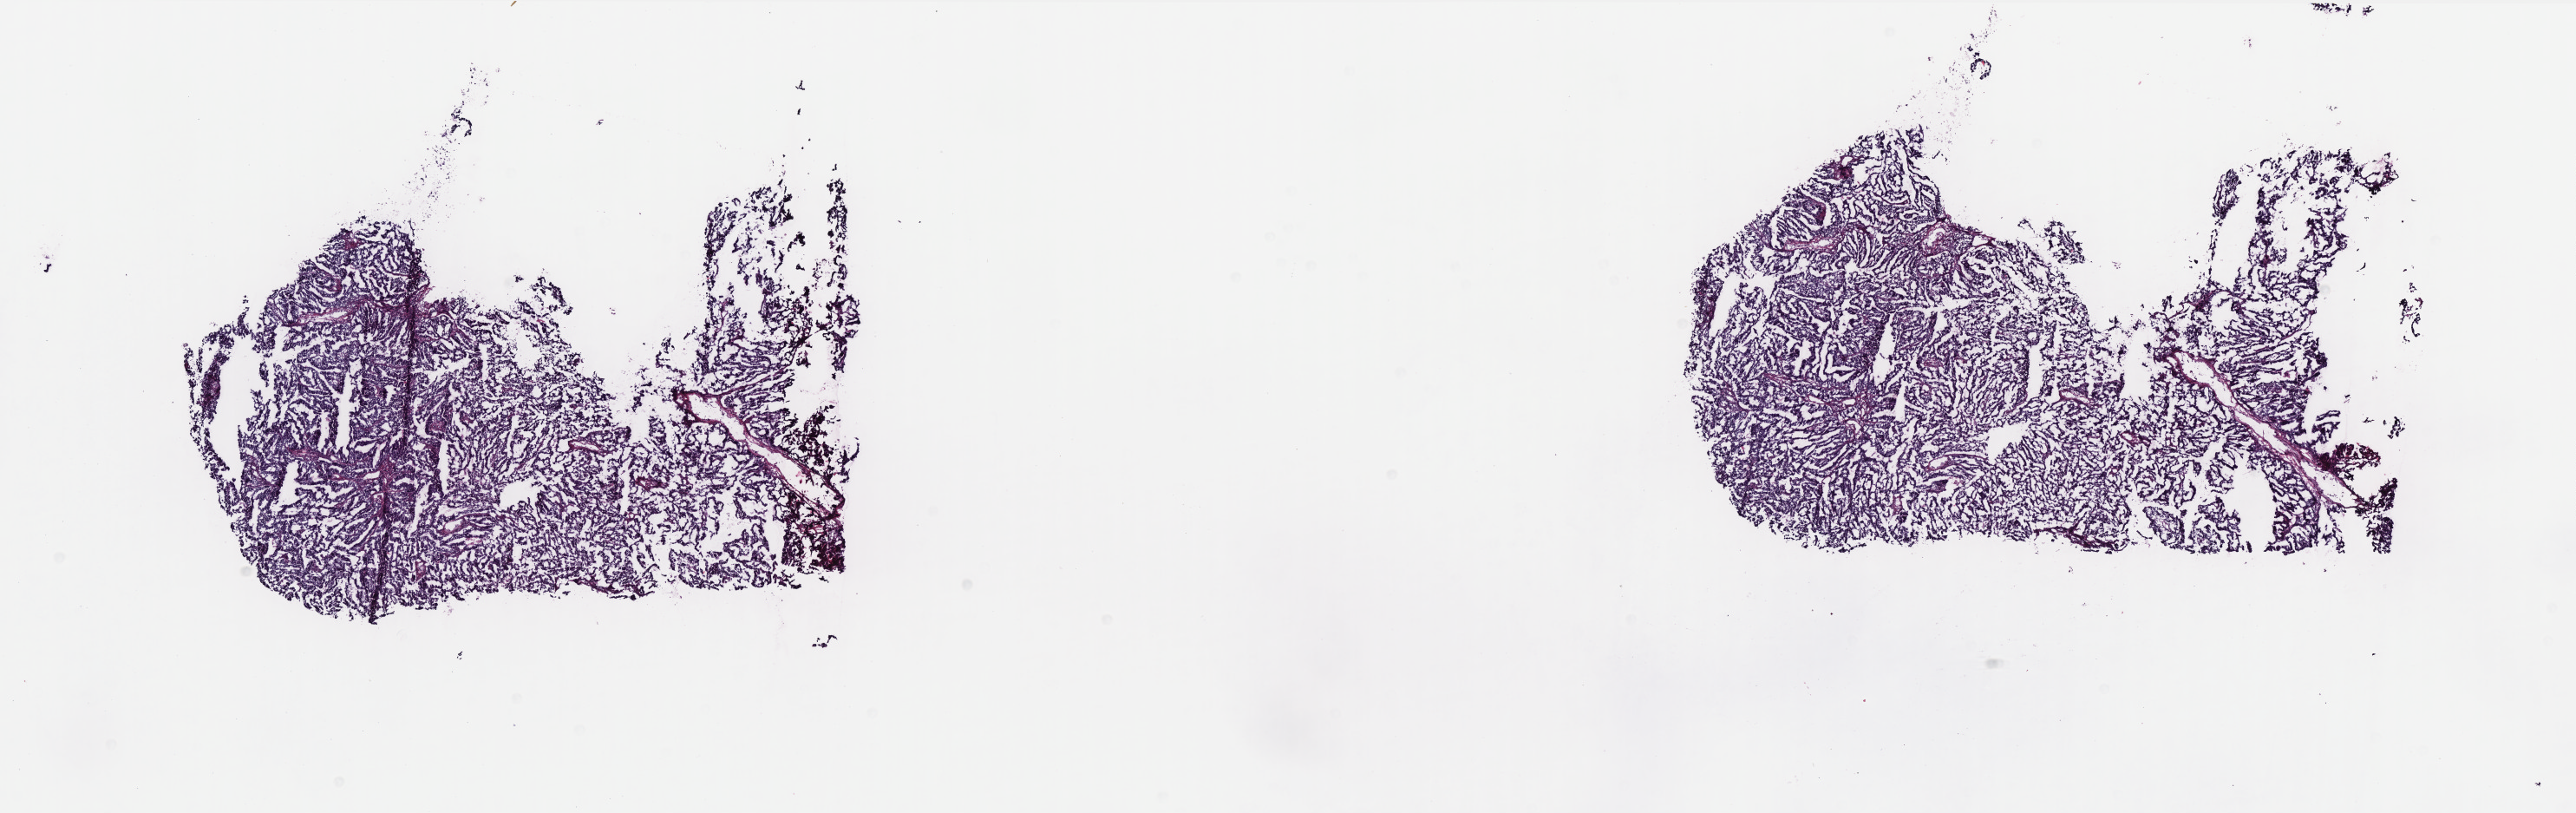
Hematoxylin and eosin (H&E) stained whole-slide image, whole scanned area (about 23.8 x 7.5 mm, acquisition: 40x scan) shown as a low-resolution overview. Frozen section. Primary tumour sample from the uterus. Patient: female, age at initial diagnosis 63 years. Histologic grade: G2 (moderately differentiated). Slide review estimates, as recorded: tumour cells 100%, tumour nuclei 90%, normal cells 0%, stromal cells 0%, necrosis 0%. Infiltration values recorded for this section: lymphocyte infiltration 1%, monocyte infiltration 0%, neutrophil infiltration 0%.
• FIGO stage: IA
• pathologic diagnosis: Endometrioid adenocarcinoma, NOS
• lymph nodes positive (case pathology): 0 of 6 examined